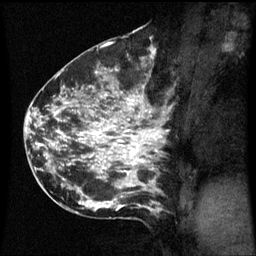
Breast MRI (dynamic contrast-enhanced), one sagittal slice. Slice 35 of 60 in the series (ordered by position). Dynamic contrast-enhanced series, image 2 of 3 at this slice position (ordered by acquisition). 1.5 T. TE 4.2 ms, TR 8.9 ms. 2.1 mm slice thickness. 256 × 256 image matrix, field of view 200 × 200 mm. Female patient, age 42 years. From the clinical record (not read from this slice): setting: breast cancer imaged before/during neoadjuvant chemotherapy; receptor status: HER2-positive.
Structures marked on this image (semi-automatic segmentation, software-assisted and operator-edited):
- analysis volume of interest (the breast-tissue region the enhancement analysis was run in; not a lesion): bounding box [x1, y1, x2, y2] px = [66, 82, 173, 193]
- tumour enhancement mask (voxels above the 70 % enhancement threshold inside the analysis volume of interest): [80, 96, 163, 187]